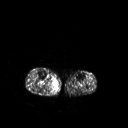
FDG PET of an extremity soft-tissue mass (from a PET/CT study), one axial slice; slice 147 of 267 in the series (ordered by position); 128 × 128 image matrix, field of view 500 × 500 mm. Male patient, age 69 years. From the clinical record (not read from this slice): histological type: pleiomorphic liposarcoma; grade: high; site of the primary tumour: right calf.
Outlined on this slice (expert contour drawn on MRI and transferred to this co-registered scan by the dataset authors):
- gross tumour volume including surrounding oedema: box from (x=54, y=79) to (x=58, y=88) px